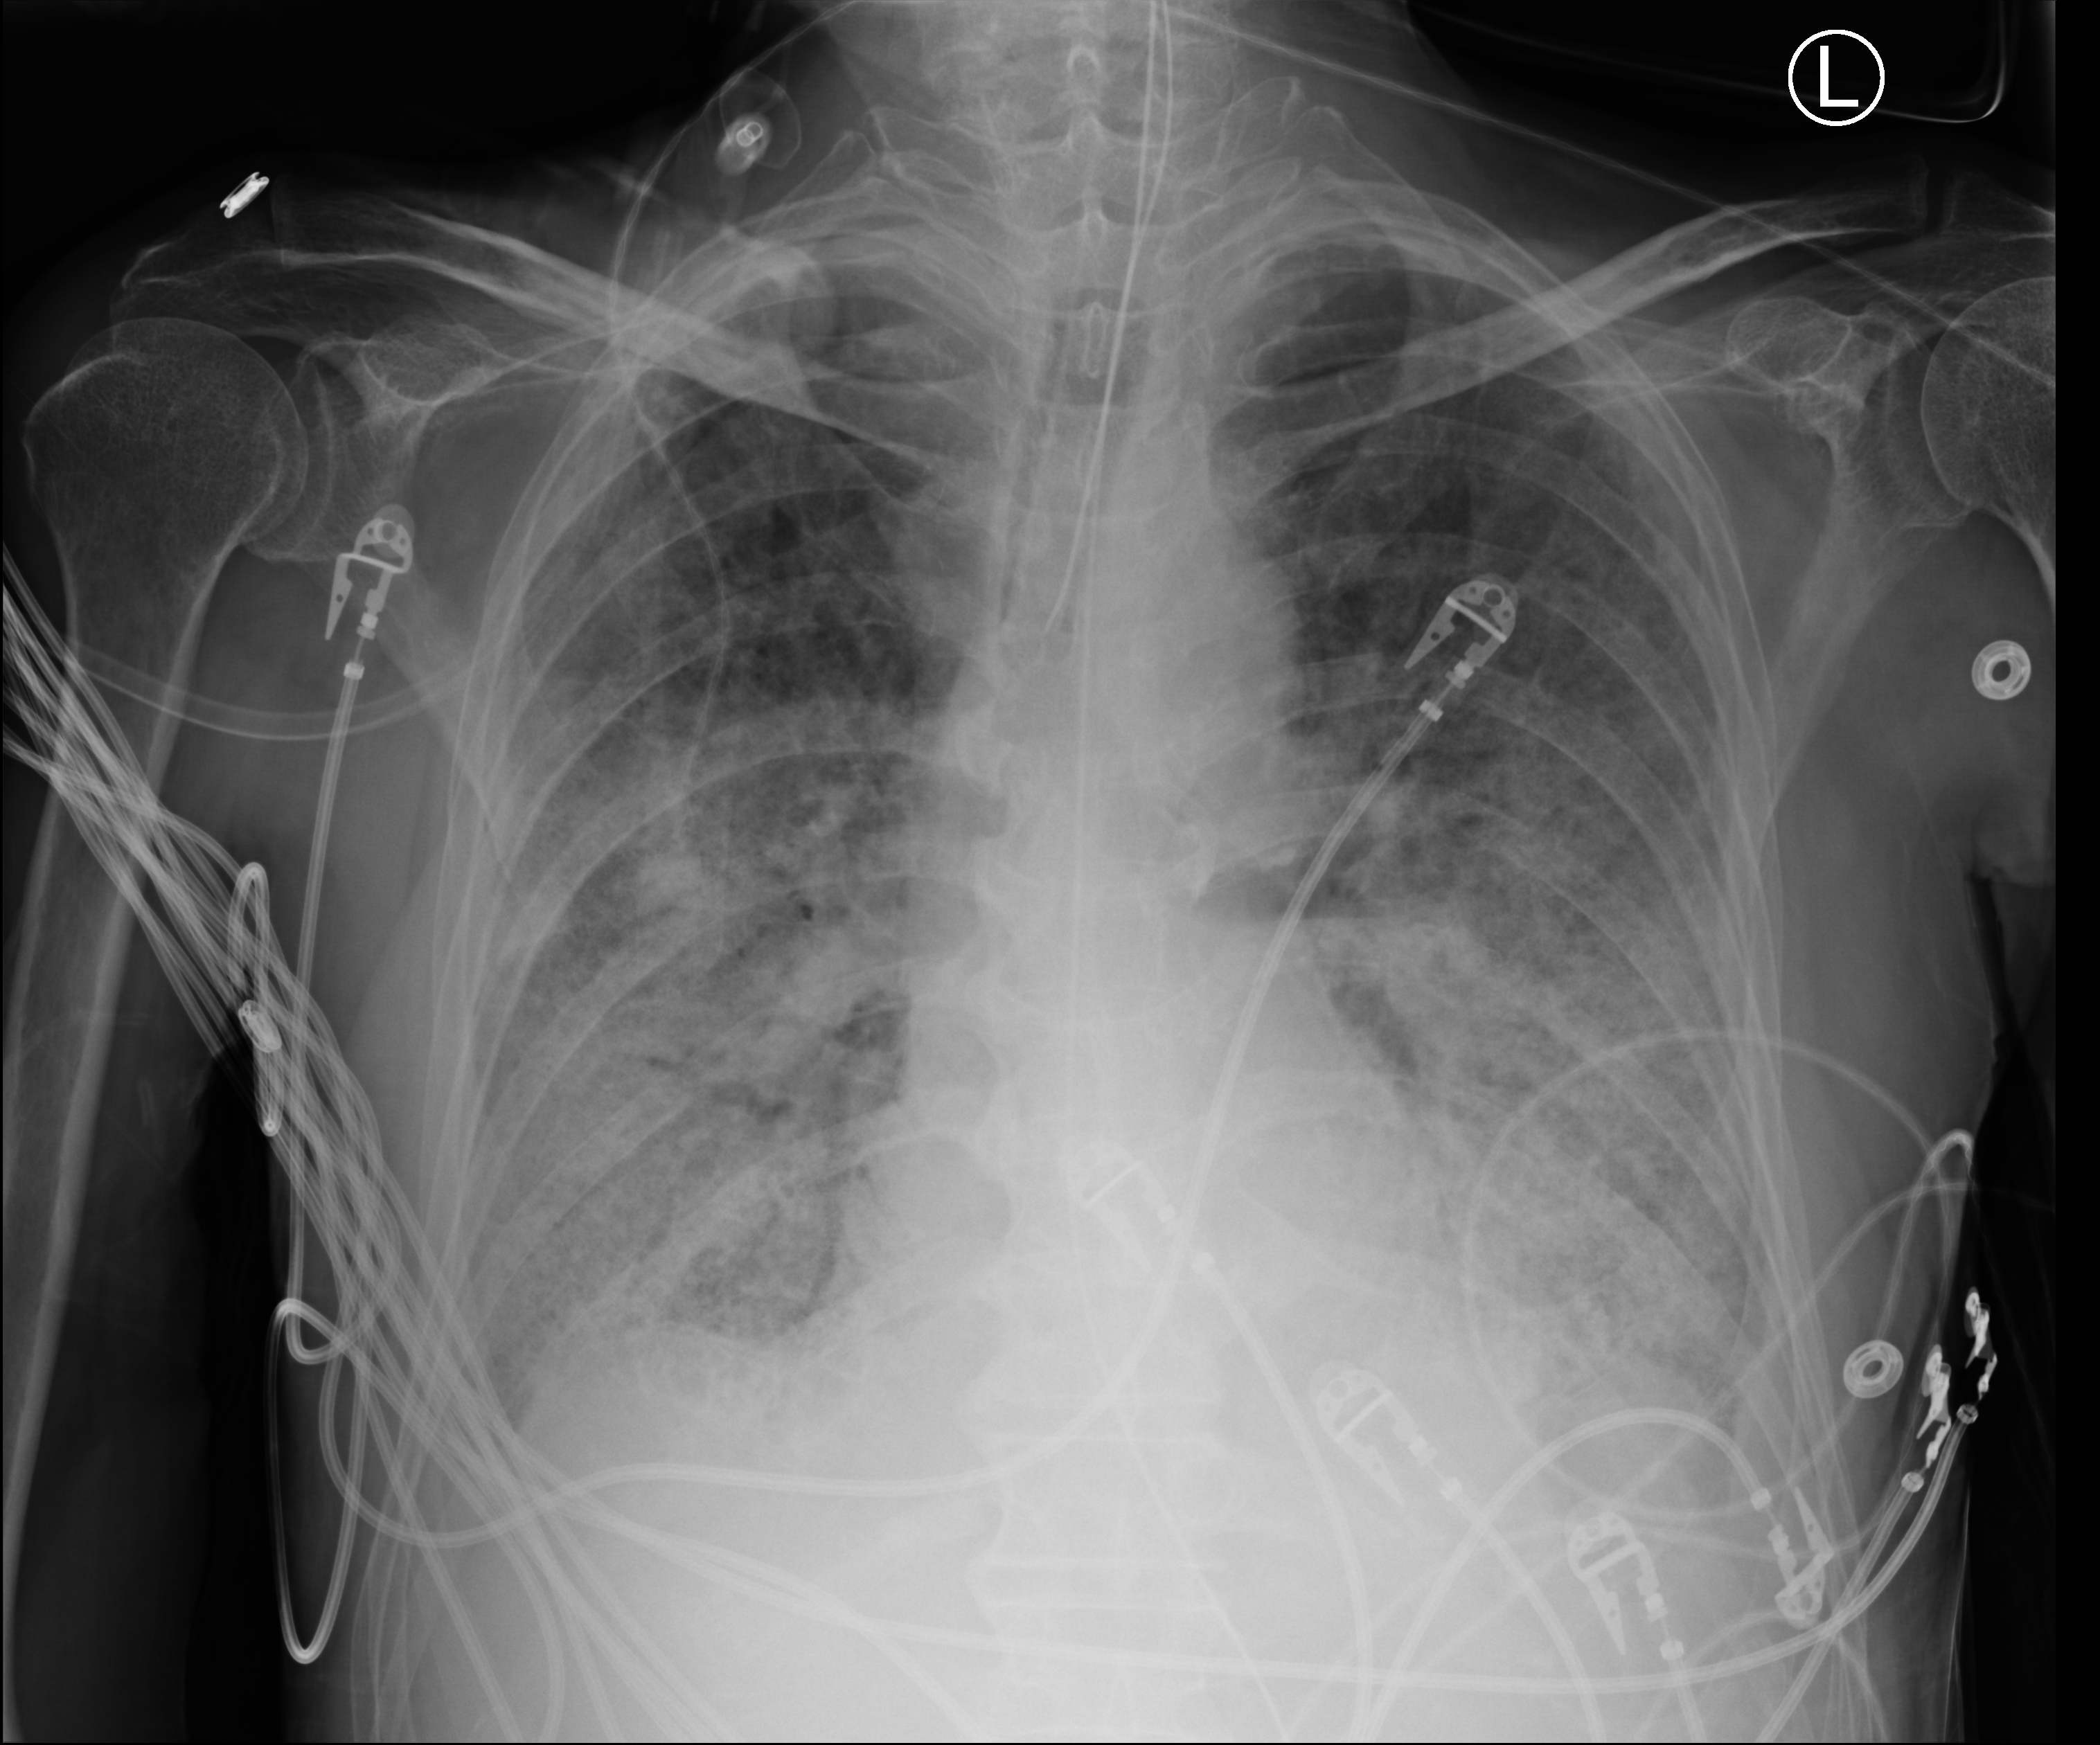
Portable chest radiograph. Male patient hospitalised with COVID-19, age 60–74 years.
From the hospital-stay record, not from the radiograph (when in the stay this image was taken is not recorded):
- mechanically ventilated during this hospital stay: yes